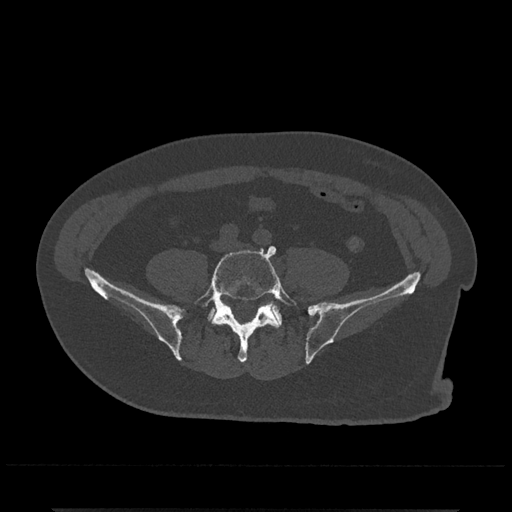
CT including the spine, one axial slice. Position 82 of 797 along the scan axis. Reconstruction kernel Br40s/3. Bone window (W 1800 / L 400 HU). 0.5 mm slice thickness. 512 × 512 image matrix, field of view 393 × 393 mm. Patient: male, 67 years. Case-level facts recorded for this patient, not image findings: primary cancer: prostate.
Outlined on this slice (semi-automatically segmented with operator editing):
- L5 vertebra: bounding box <194,246,297,363> (left, top, right, bottom; pixels)